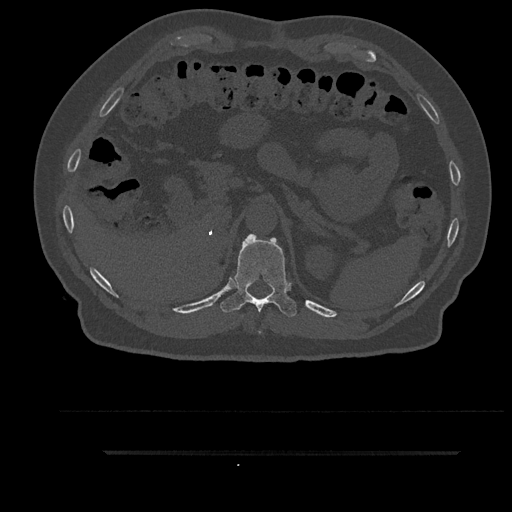
CT including the spine, one axial slice; position 308 of 797 along the scan axis; 120 kVp; bone window (W 1800 / L 400 HU); 0.5 mm slice thickness; 512 × 512 image matrix, field of view 432 × 432 mm. Male patient, age 63 years. Case-level facts recorded for this patient, not image findings: primary cancer: renal.
Annotated regions visible in this slice (semi-automatically segmented with operator editing):
- T11 vertebra: bounding box <220,234,297,333> (left, top, right, bottom; pixels)